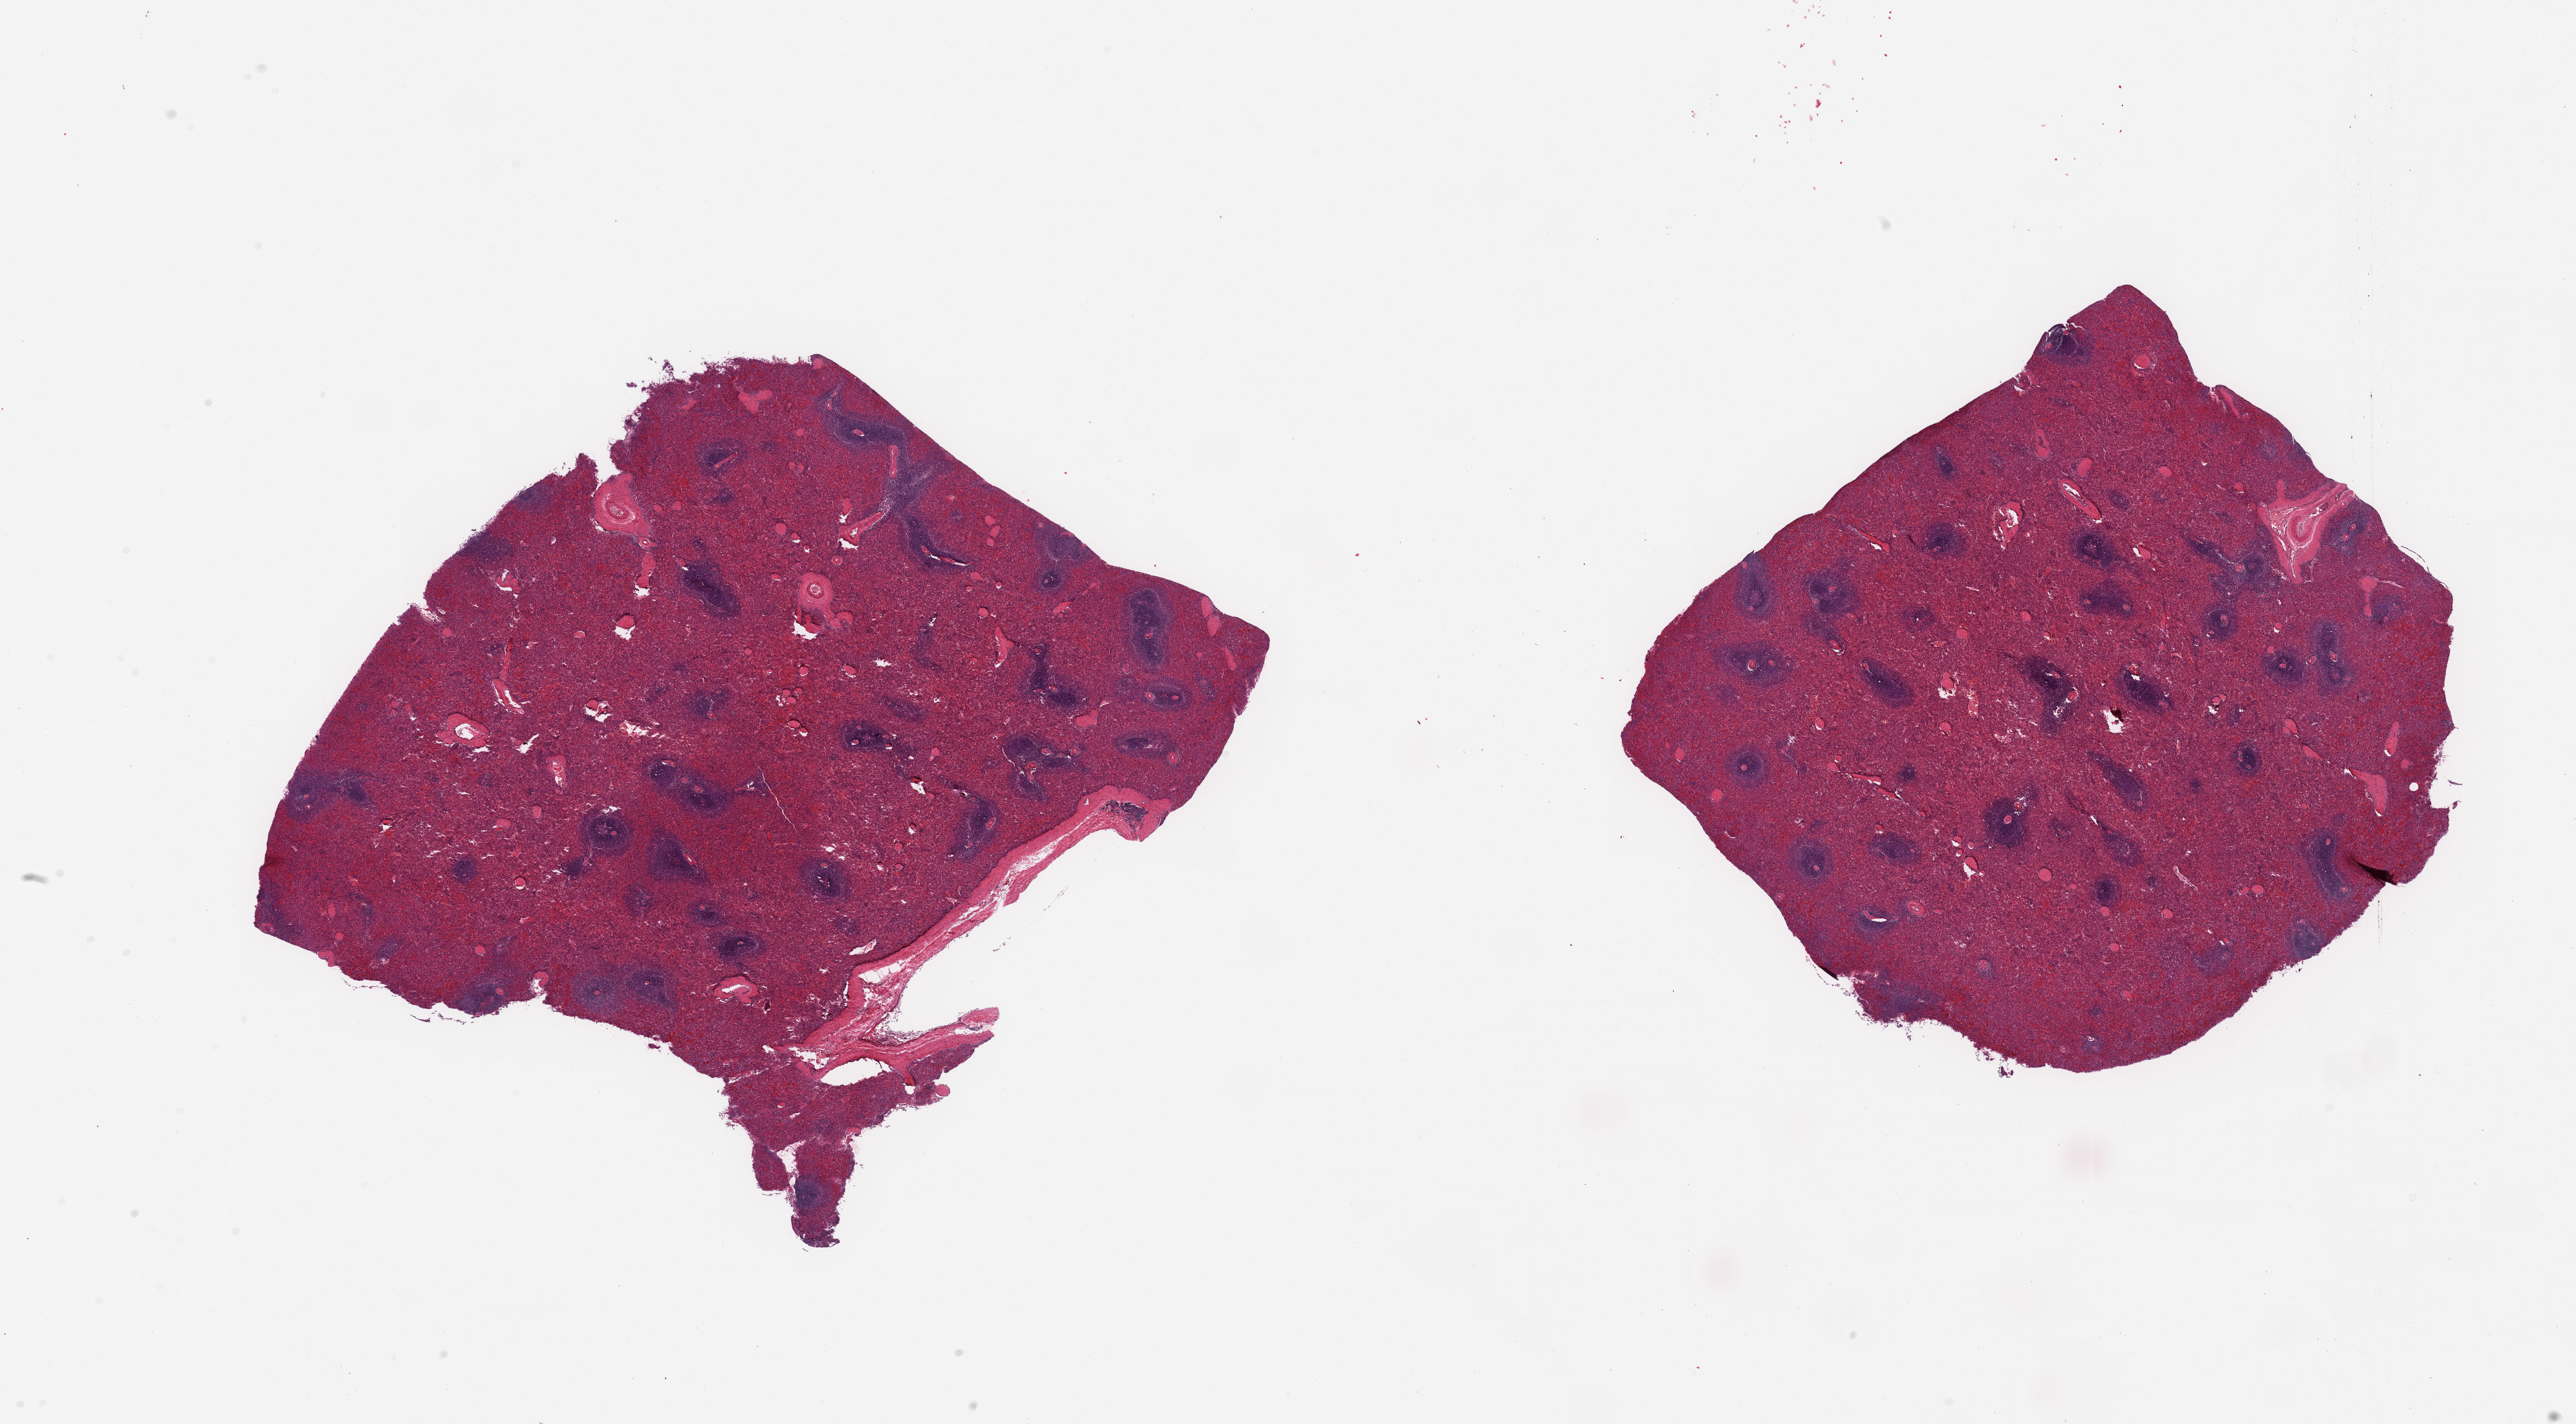
Whole-slide image, H&E stain — shown as a low-resolution overview of the whole scanned area (about 31.5 x 17.4 mm, slide scanned at 20x). PAXgene-fixed paraffin-embedded (PFPE) section. Section of spleen (target tissue). Tissue donor sample. Donor: male.
Reviewer comment on this tissue sample: 2 pieces; congestion.